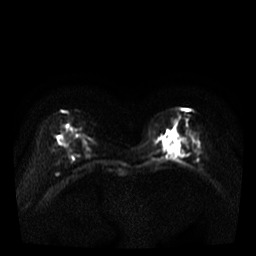
Breast MRI, one axial slice; position 12 of 35 along the scan axis; diffusion-weighted series; image 2 of 4 stored at this slice position (different b-values; order by instance number); 3 T; 5 mm slice thickness; 256 × 256 image matrix, field of view 320 × 320 mm. Female patient.
Outlined on this slice (manually delineated by an expert):
- tumour on diffusion-weighted imaging: bounding box (x1, y1, x2, y2) in pixels: (169, 144, 180, 156)